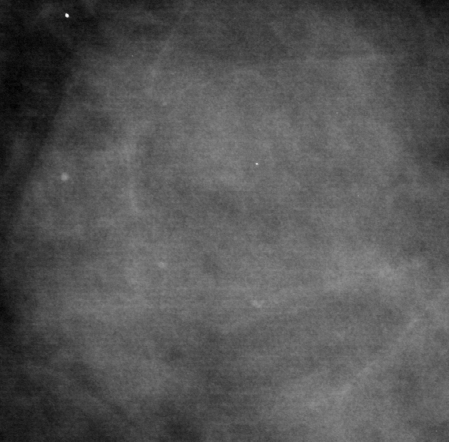
Crop from a digitized film mammogram around one marked abnormality, left breast, MLO view.
- Mass, shape lobulated, margins obscured; BI-RADS assessment category 4; subtlety rating 5 on a 1 (subtle) to 5 (obvious) scale; pathology (as recorded): benign.